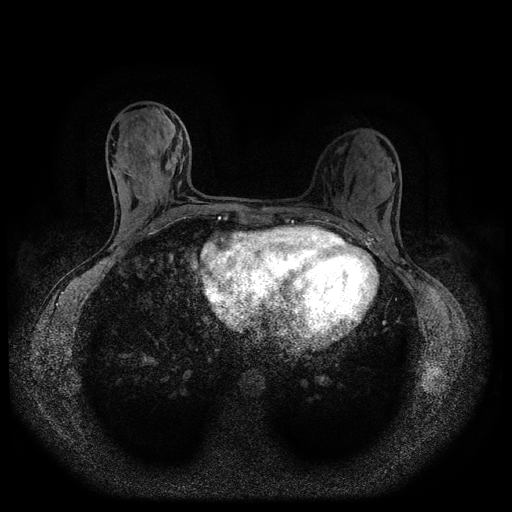
Breast MRI (dynamic contrast-enhanced, multi-phase), one axial slice; position 42 of 116 along the scan axis; dynamic contrast-enhanced series, time point 2 of 5 at this slice position (early post-contrast); 1.5 T; TE 2.7 ms, TR 5.4 ms; 512 × 512 image matrix, field of view 330 × 330 mm. Female patient, age 32 years.
Annotated regions visible in this slice (semi-automatically segmented with operator editing):
- breast lesion (labelled benign in the annotation): box from (x=165, y=156) to (x=173, y=172) px